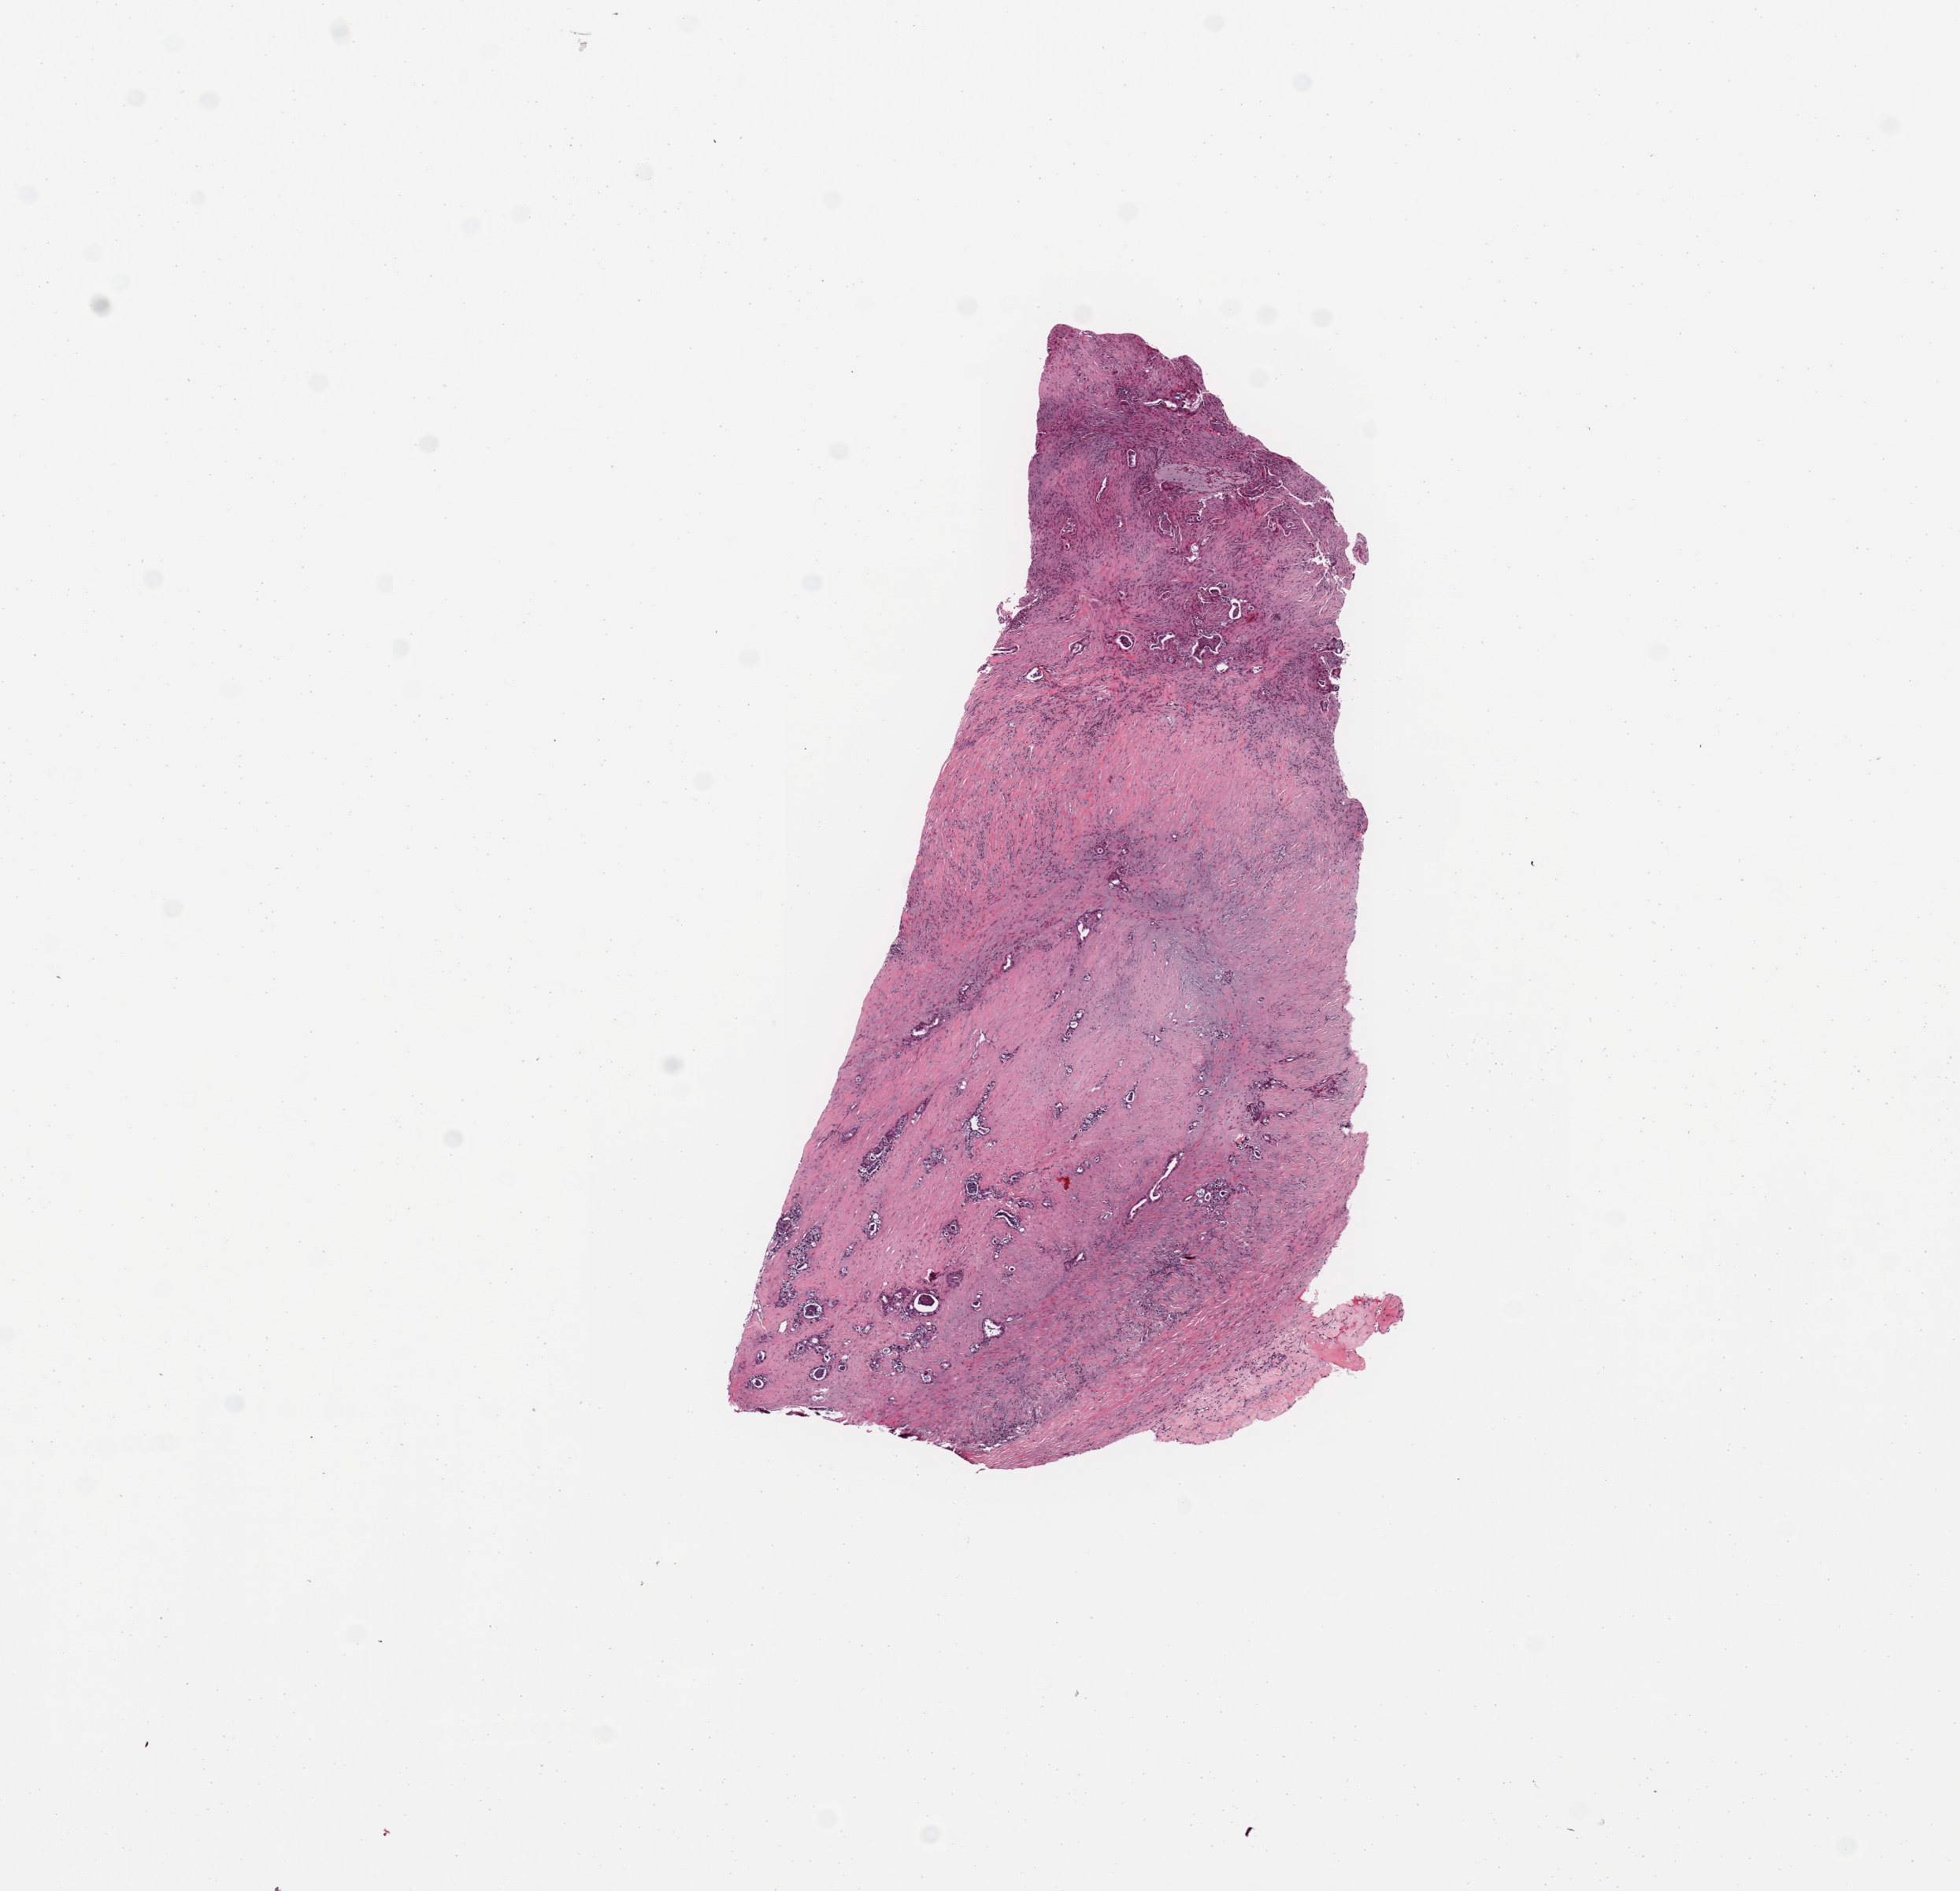
Whole-slide histology image, Hematoxylin and eosin (H&E) stained, whole scanned area (about 9.8 x 9.5 mm) shown as a low-resolution overview, tumour tissue sample, sampled site: pancreas. Female, 73 y/o. Pathologist review of this section (percent, as recorded): tumour nuclei 20%, necrosis 2%.
Diagnosis: Infiltrating duct carcinoma, NOS.